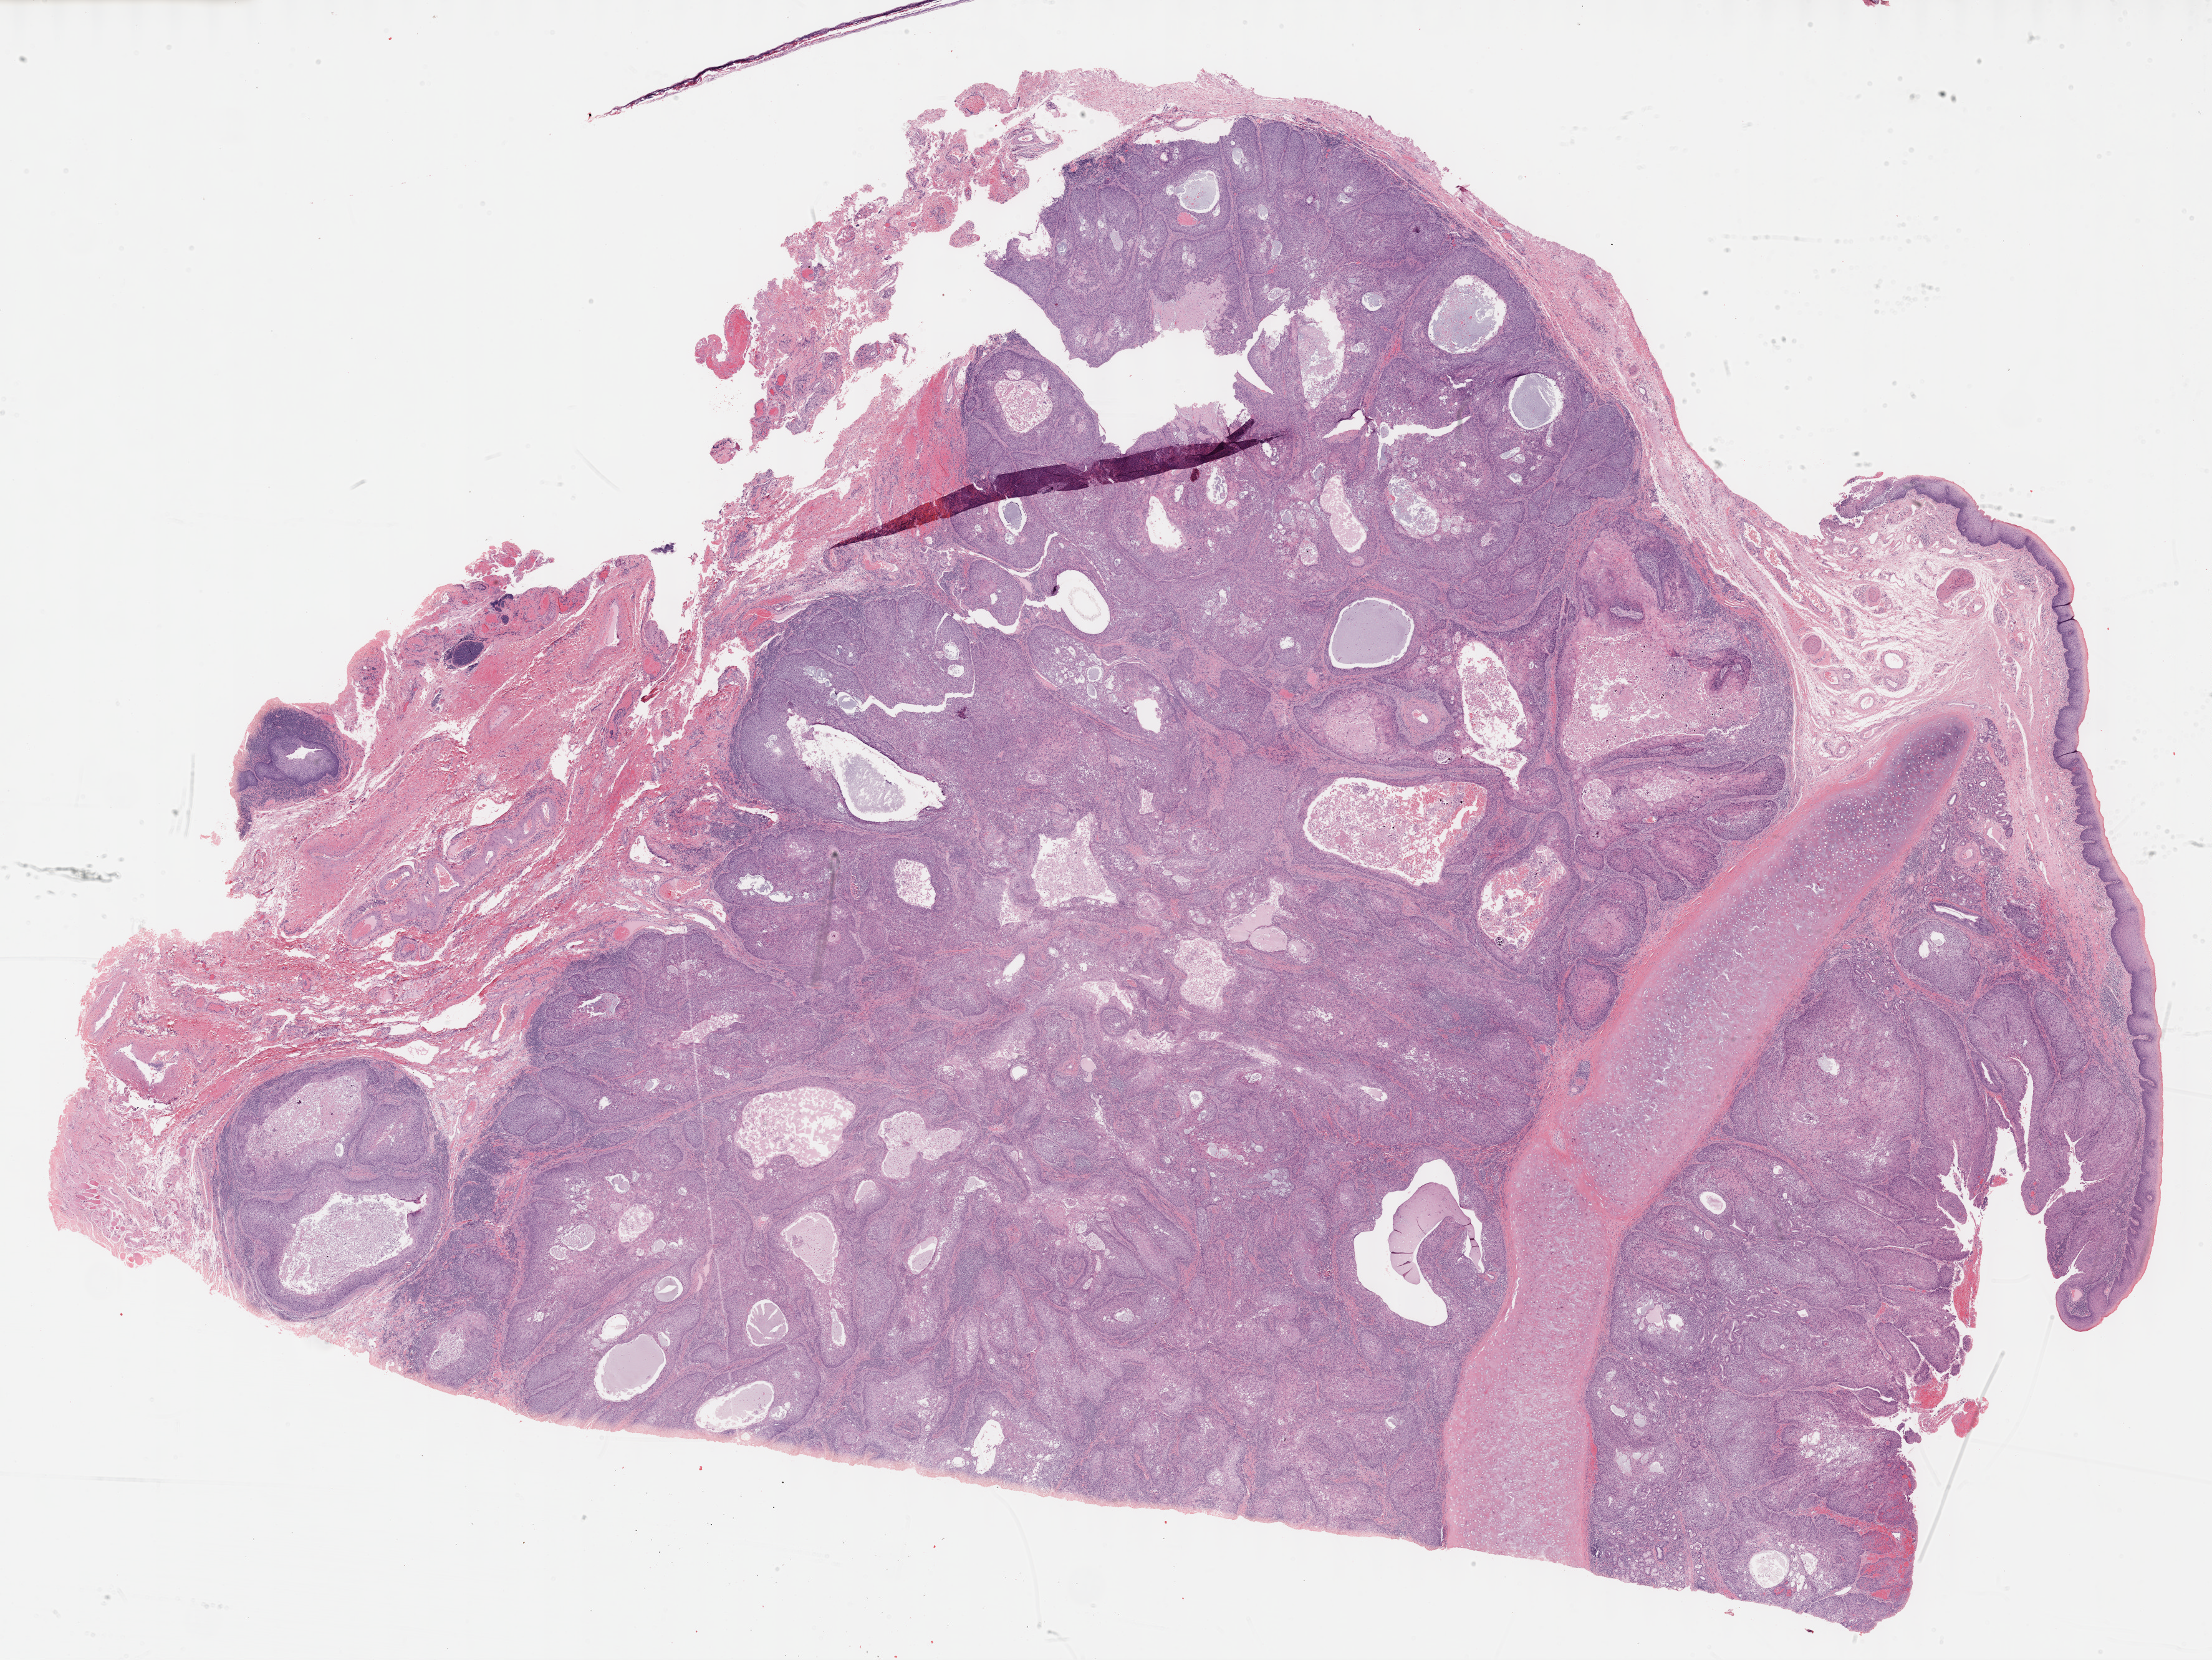
Whole-slide histology image, H&E — a low-resolution overview of the entire scanned area, about 28.7 x 21.5 mm (acquisition: 40x scan). Formalin-fixed paraffin-embedded (FFPE) diagnostic section. Sample: primary tumour, head and neck. Patient: male, age at initial diagnosis 65 years. Histologic grade: G2 (moderately differentiated).
Diagnosis: Squamous cell carcinoma, NOS (larynx, NOS).